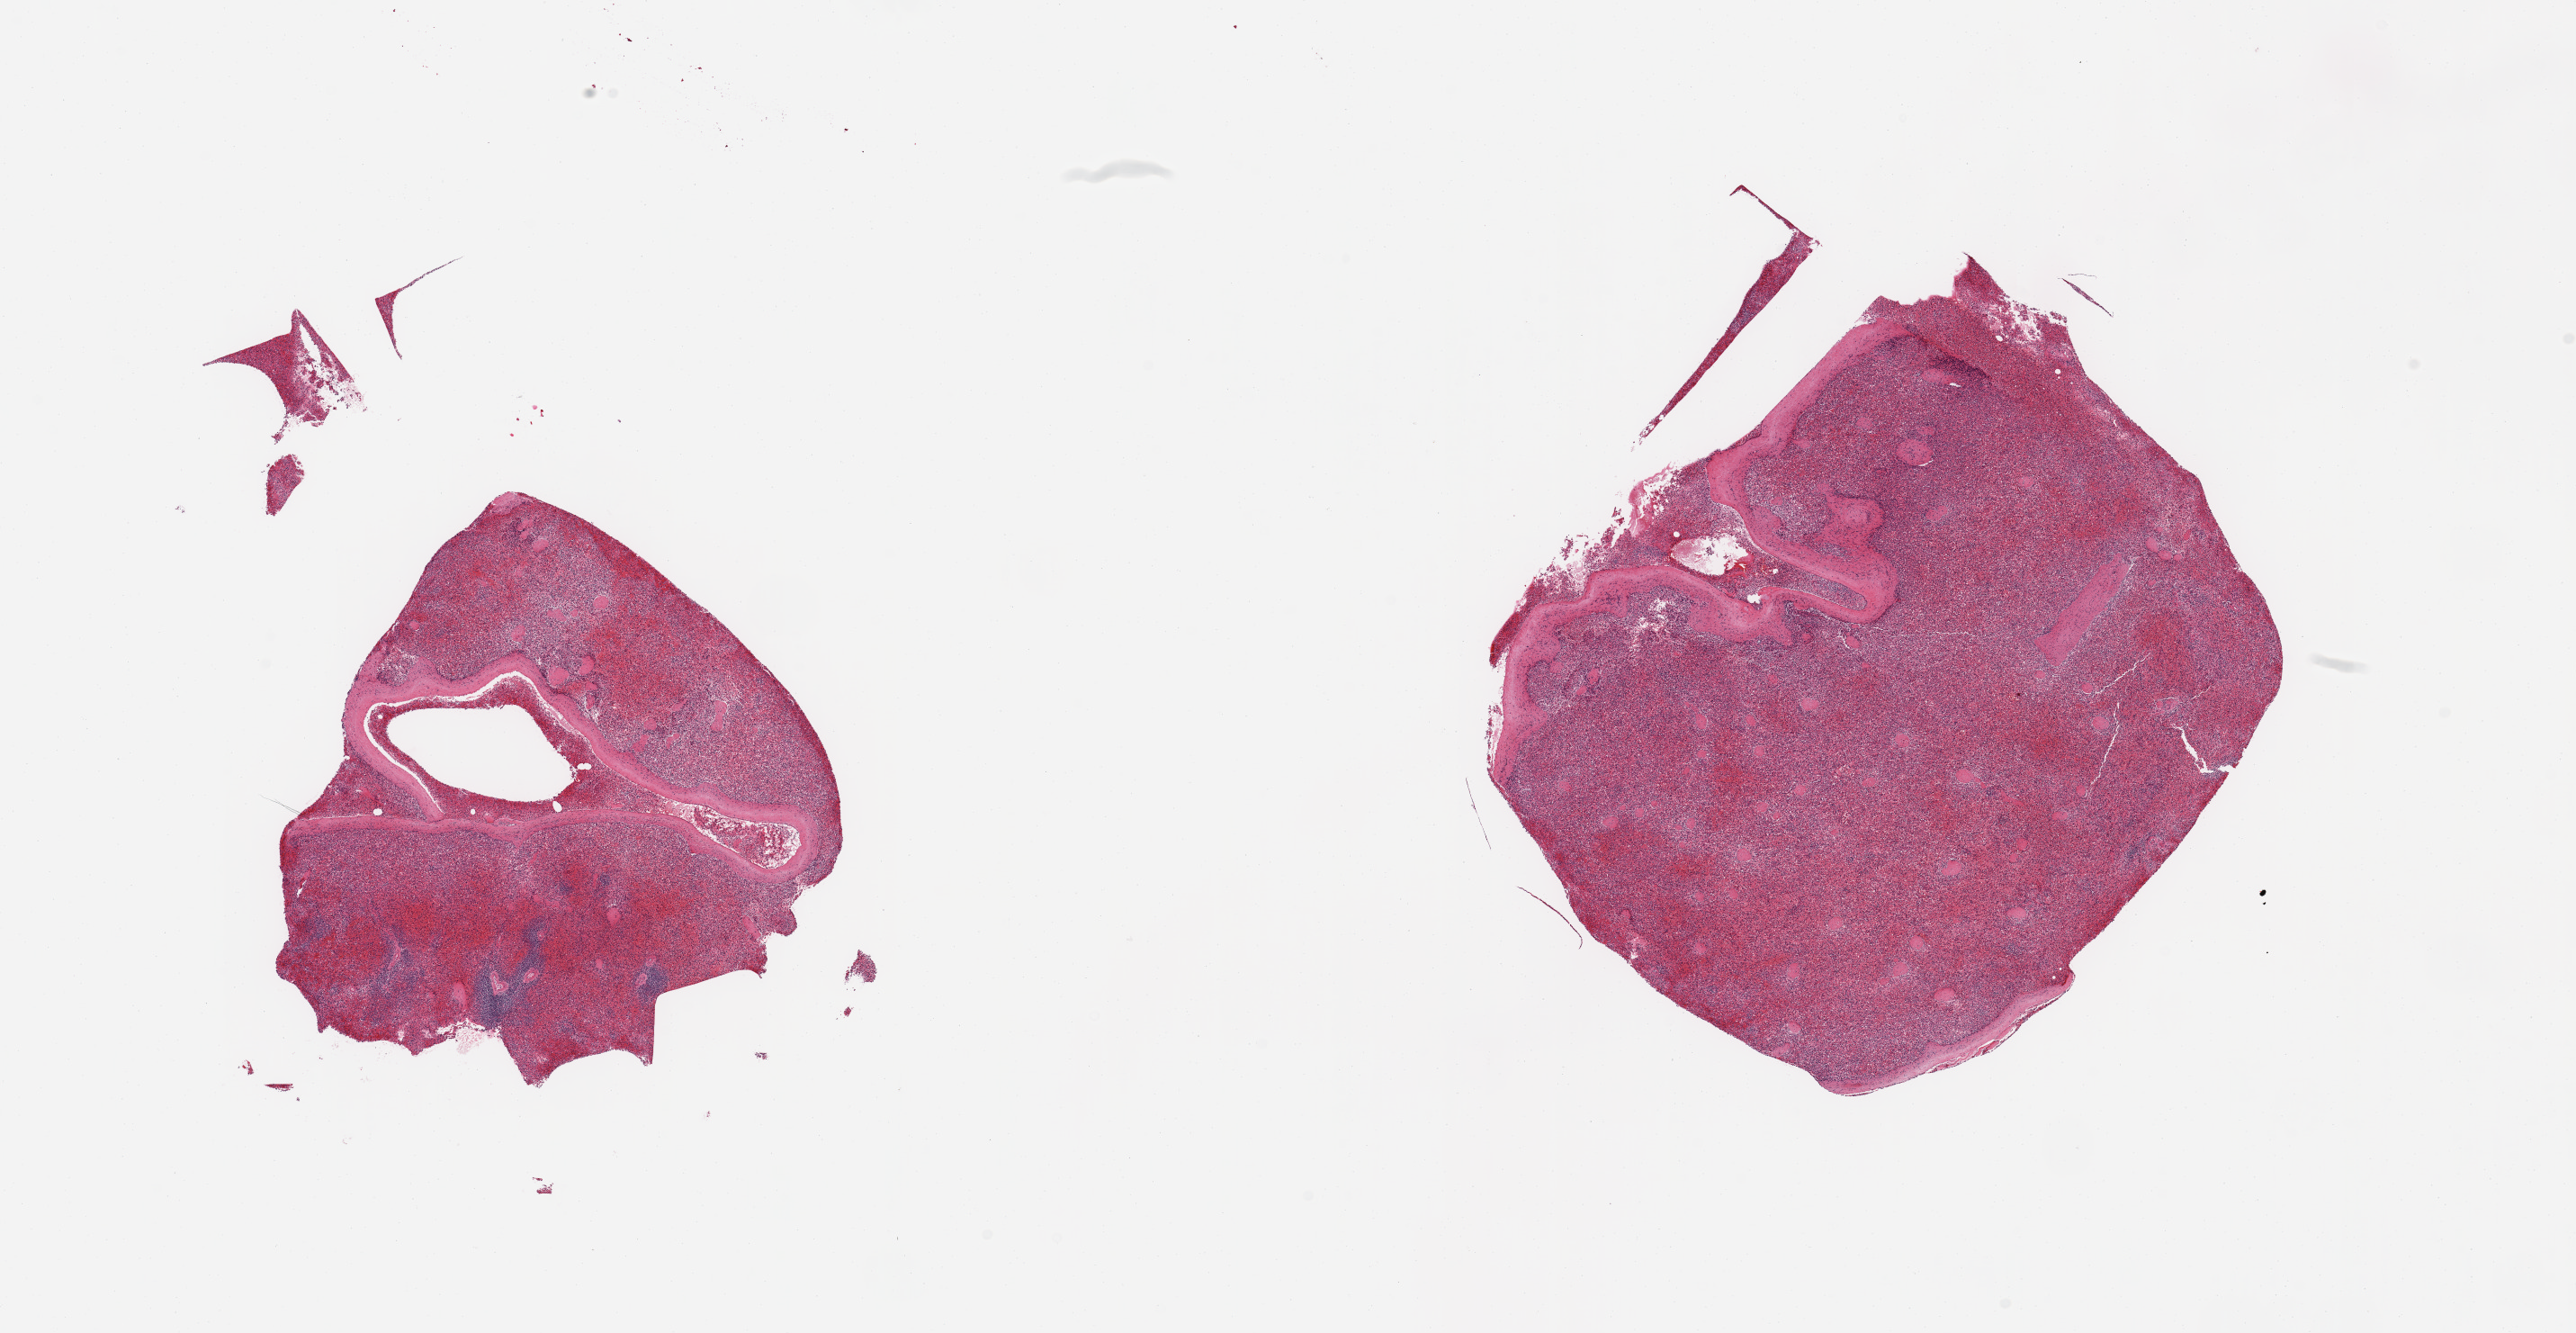
Digitized hematoxylin and eosin (H&E)-stained section, brightfield — shown as a low-resolution overview of the whole scanned area (about 22.6 x 11.7 mm, from a 20x scan); PAXgene-fixed, paraffin-embedded tissue; target tissue: spleen; donor tissue sample. Donor sex: female.
- review note (as recorded): 2 pieces, moderate congestion